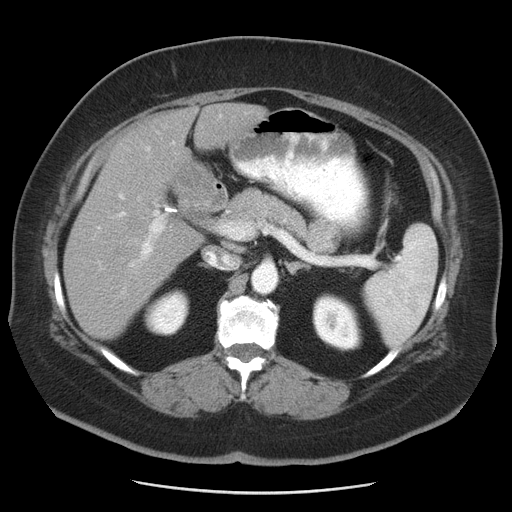
Contrast-enhanced abdominal CT, one axial slice. 120 kVp. Intravenous contrast given. Soft-tissue window (W 400 / L 40 HU). 5 mm slice thickness. 512 × 512 image matrix. Female patient, age 52 years. From the clinical record (not read from this slice): diagnosis: colorectal cancer liver metastases, imaged before liver resection; multiple liver metastases: yes; largest metastasis: 2.5 cm; chemotherapy before resection: no.
Annotated regions visible in this slice (outlined manually by an expert reader):
- liver: box from (x=63, y=104) to (x=266, y=340) px
- planned liver remnant (the part of the liver to remain after resection): (x=63, y=197)–(x=202, y=340)
- portal vein (with intrahepatic branches): (x=92, y=146)–(x=171, y=272)